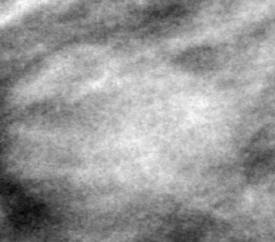
Cropped region of a digitized screen-film mammogram centred on a radiologist-marked abnormality, left breast, MLO view, BI-RADS breast density category 2 (scale 1–4).
Mass, shape oval, margins obscured; BI-RADS assessment category 3; subtlety rating 3 on a 1 (subtle) to 5 (obvious) scale; pathology result (as recorded, not read from the image): benign.